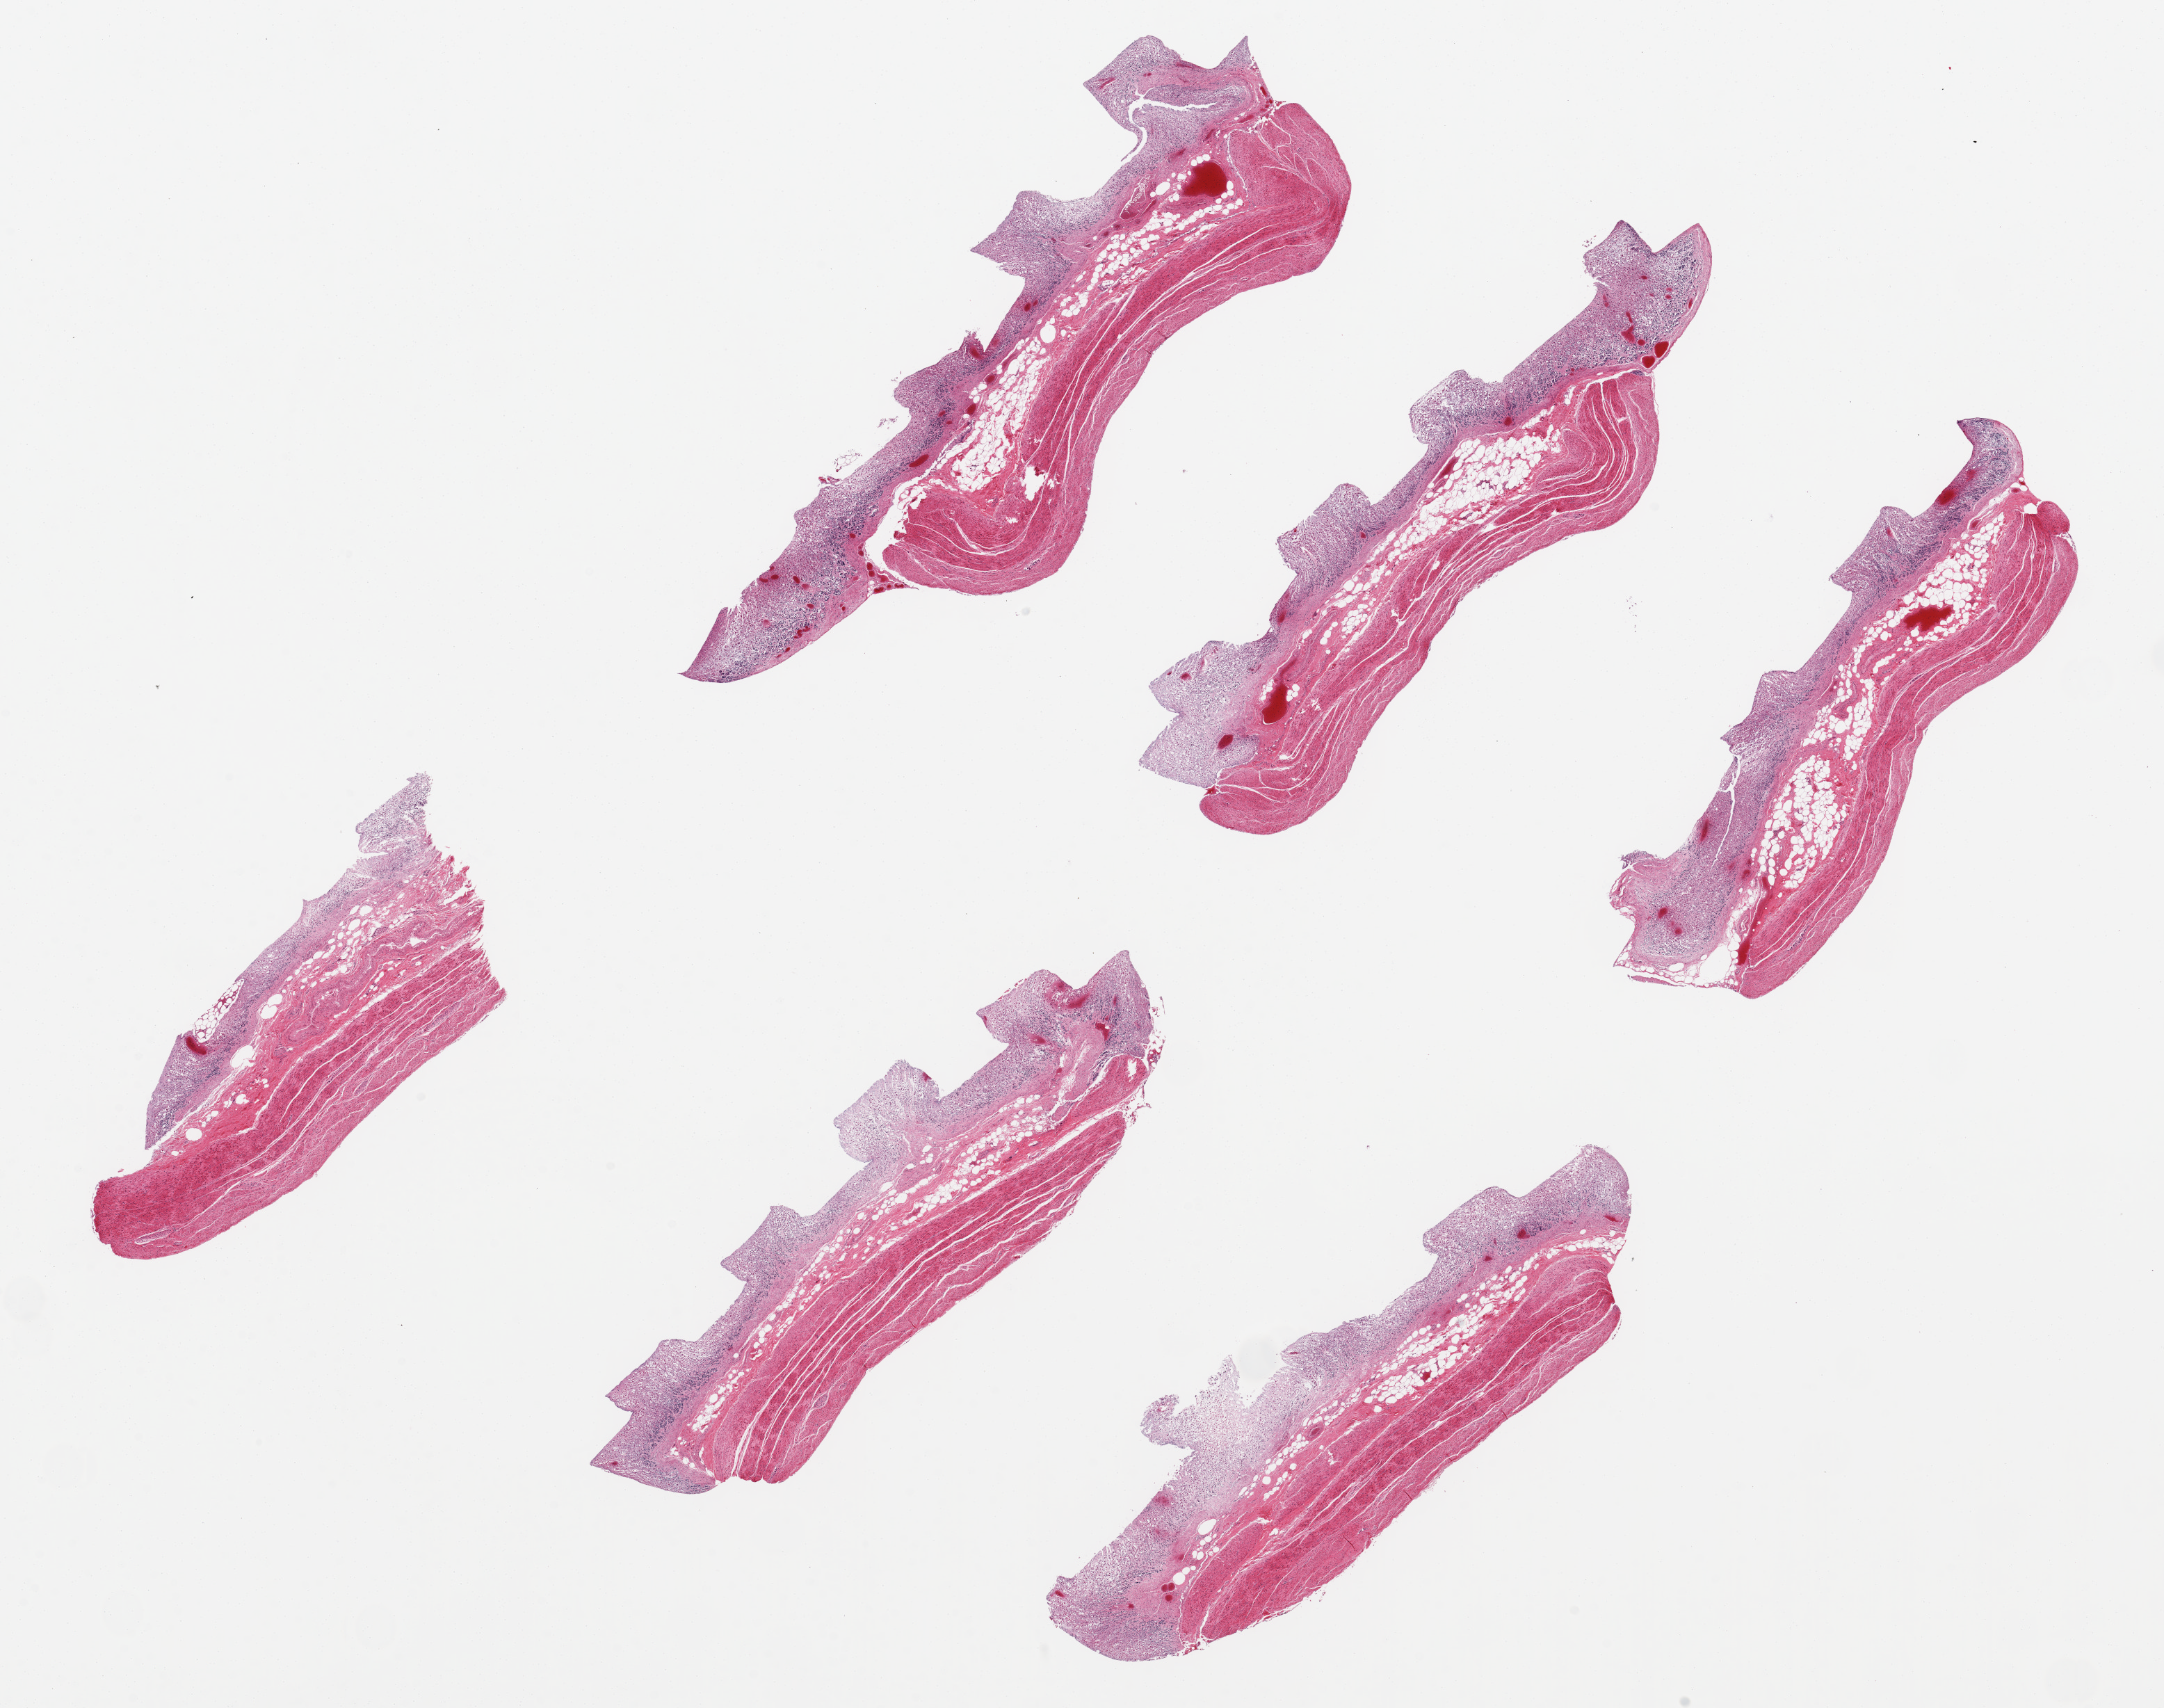
Digitized hematoxylin and eosin (H&E)-stained section, brightfield — low-resolution overview of the scanned area, about 24.6 x 19.4 mm. PAXgene-fixed paraffin-embedded (PFPE) section. Section of stomach (target tissue). Donor tissue sample. Female donor.
Pathologist's review note for this sample: 6 pieces, ~8x2mm. Mucosa with near-total autolysis and/or sloughed, ~30% of thickness.